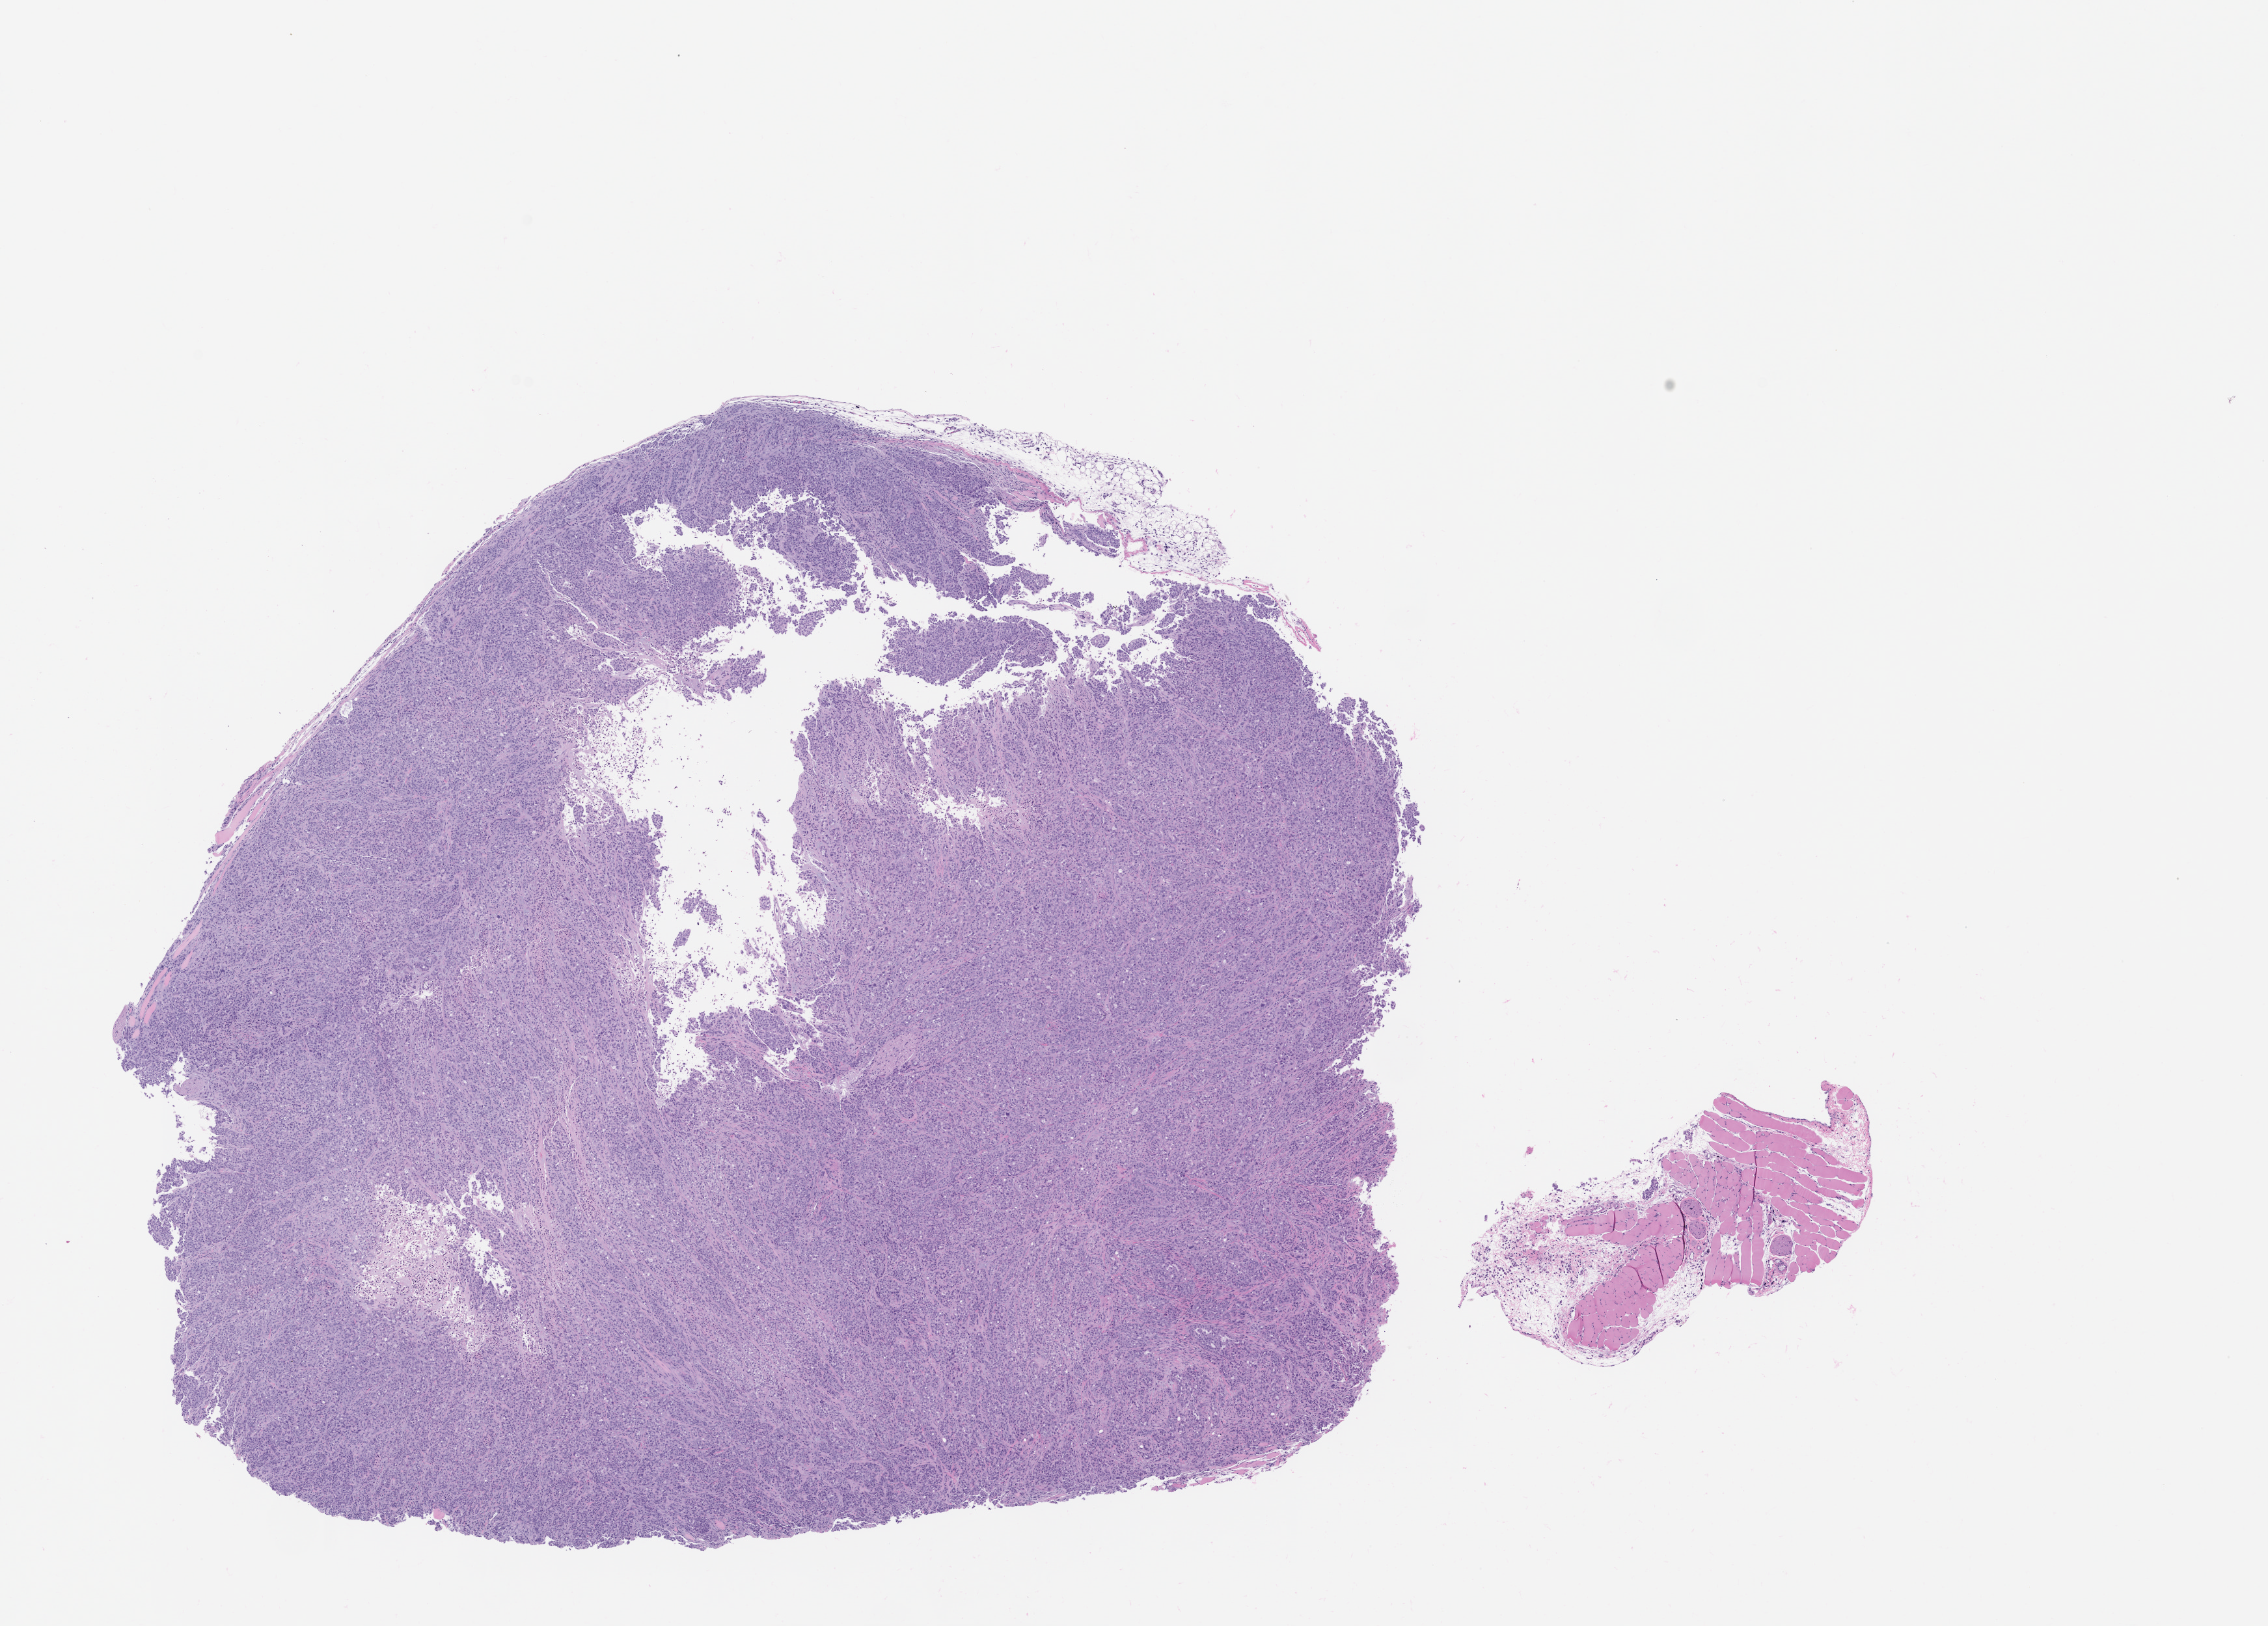
Whole-slide image, haematoxylin and eosin: patient-derived xenograft (human tumor grown in a mouse), passage 0, low-resolution overview of the scanned area, about 14.0 x 10.0 mm; formalin-fixed paraffin-embedded section; tumor site category: lung.
Originating patient diagnosis: Lung Adenocarcinoma.